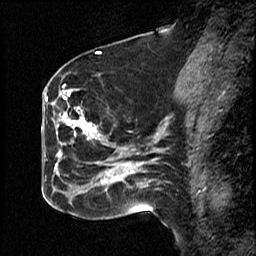
Breast MRI (dynamic contrast-enhanced), one sagittal slice; position 25 of 50 along the scan axis; dynamic contrast-enhanced study with each time point stored as its own series, time point 2 of 4 at this slice position (early post-contrast, ordered by acquisition time); 1.5 T; TE 4.2 ms, TR 18.5 ms; 3 mm slice thickness; 256 × 256 image matrix, field of view 200 × 200 mm. Patient: female, 44 years. Case-level facts recorded for this patient, not image findings: setting: breast cancer imaged before/during neoadjuvant chemotherapy; receptor status: HR-positive, HER2-negative.
Structures marked on this image (semi-automatically segmented with operator editing):
- analysis volume of interest (the breast-tissue region the enhancement analysis was run in; not a lesion): bounding box (x1, y1, x2, y2) in pixels: (59, 89, 114, 206)
- tumour enhancement mask (voxels above the 100 % enhancement threshold inside the analysis volume of interest): (59, 90, 114, 183)